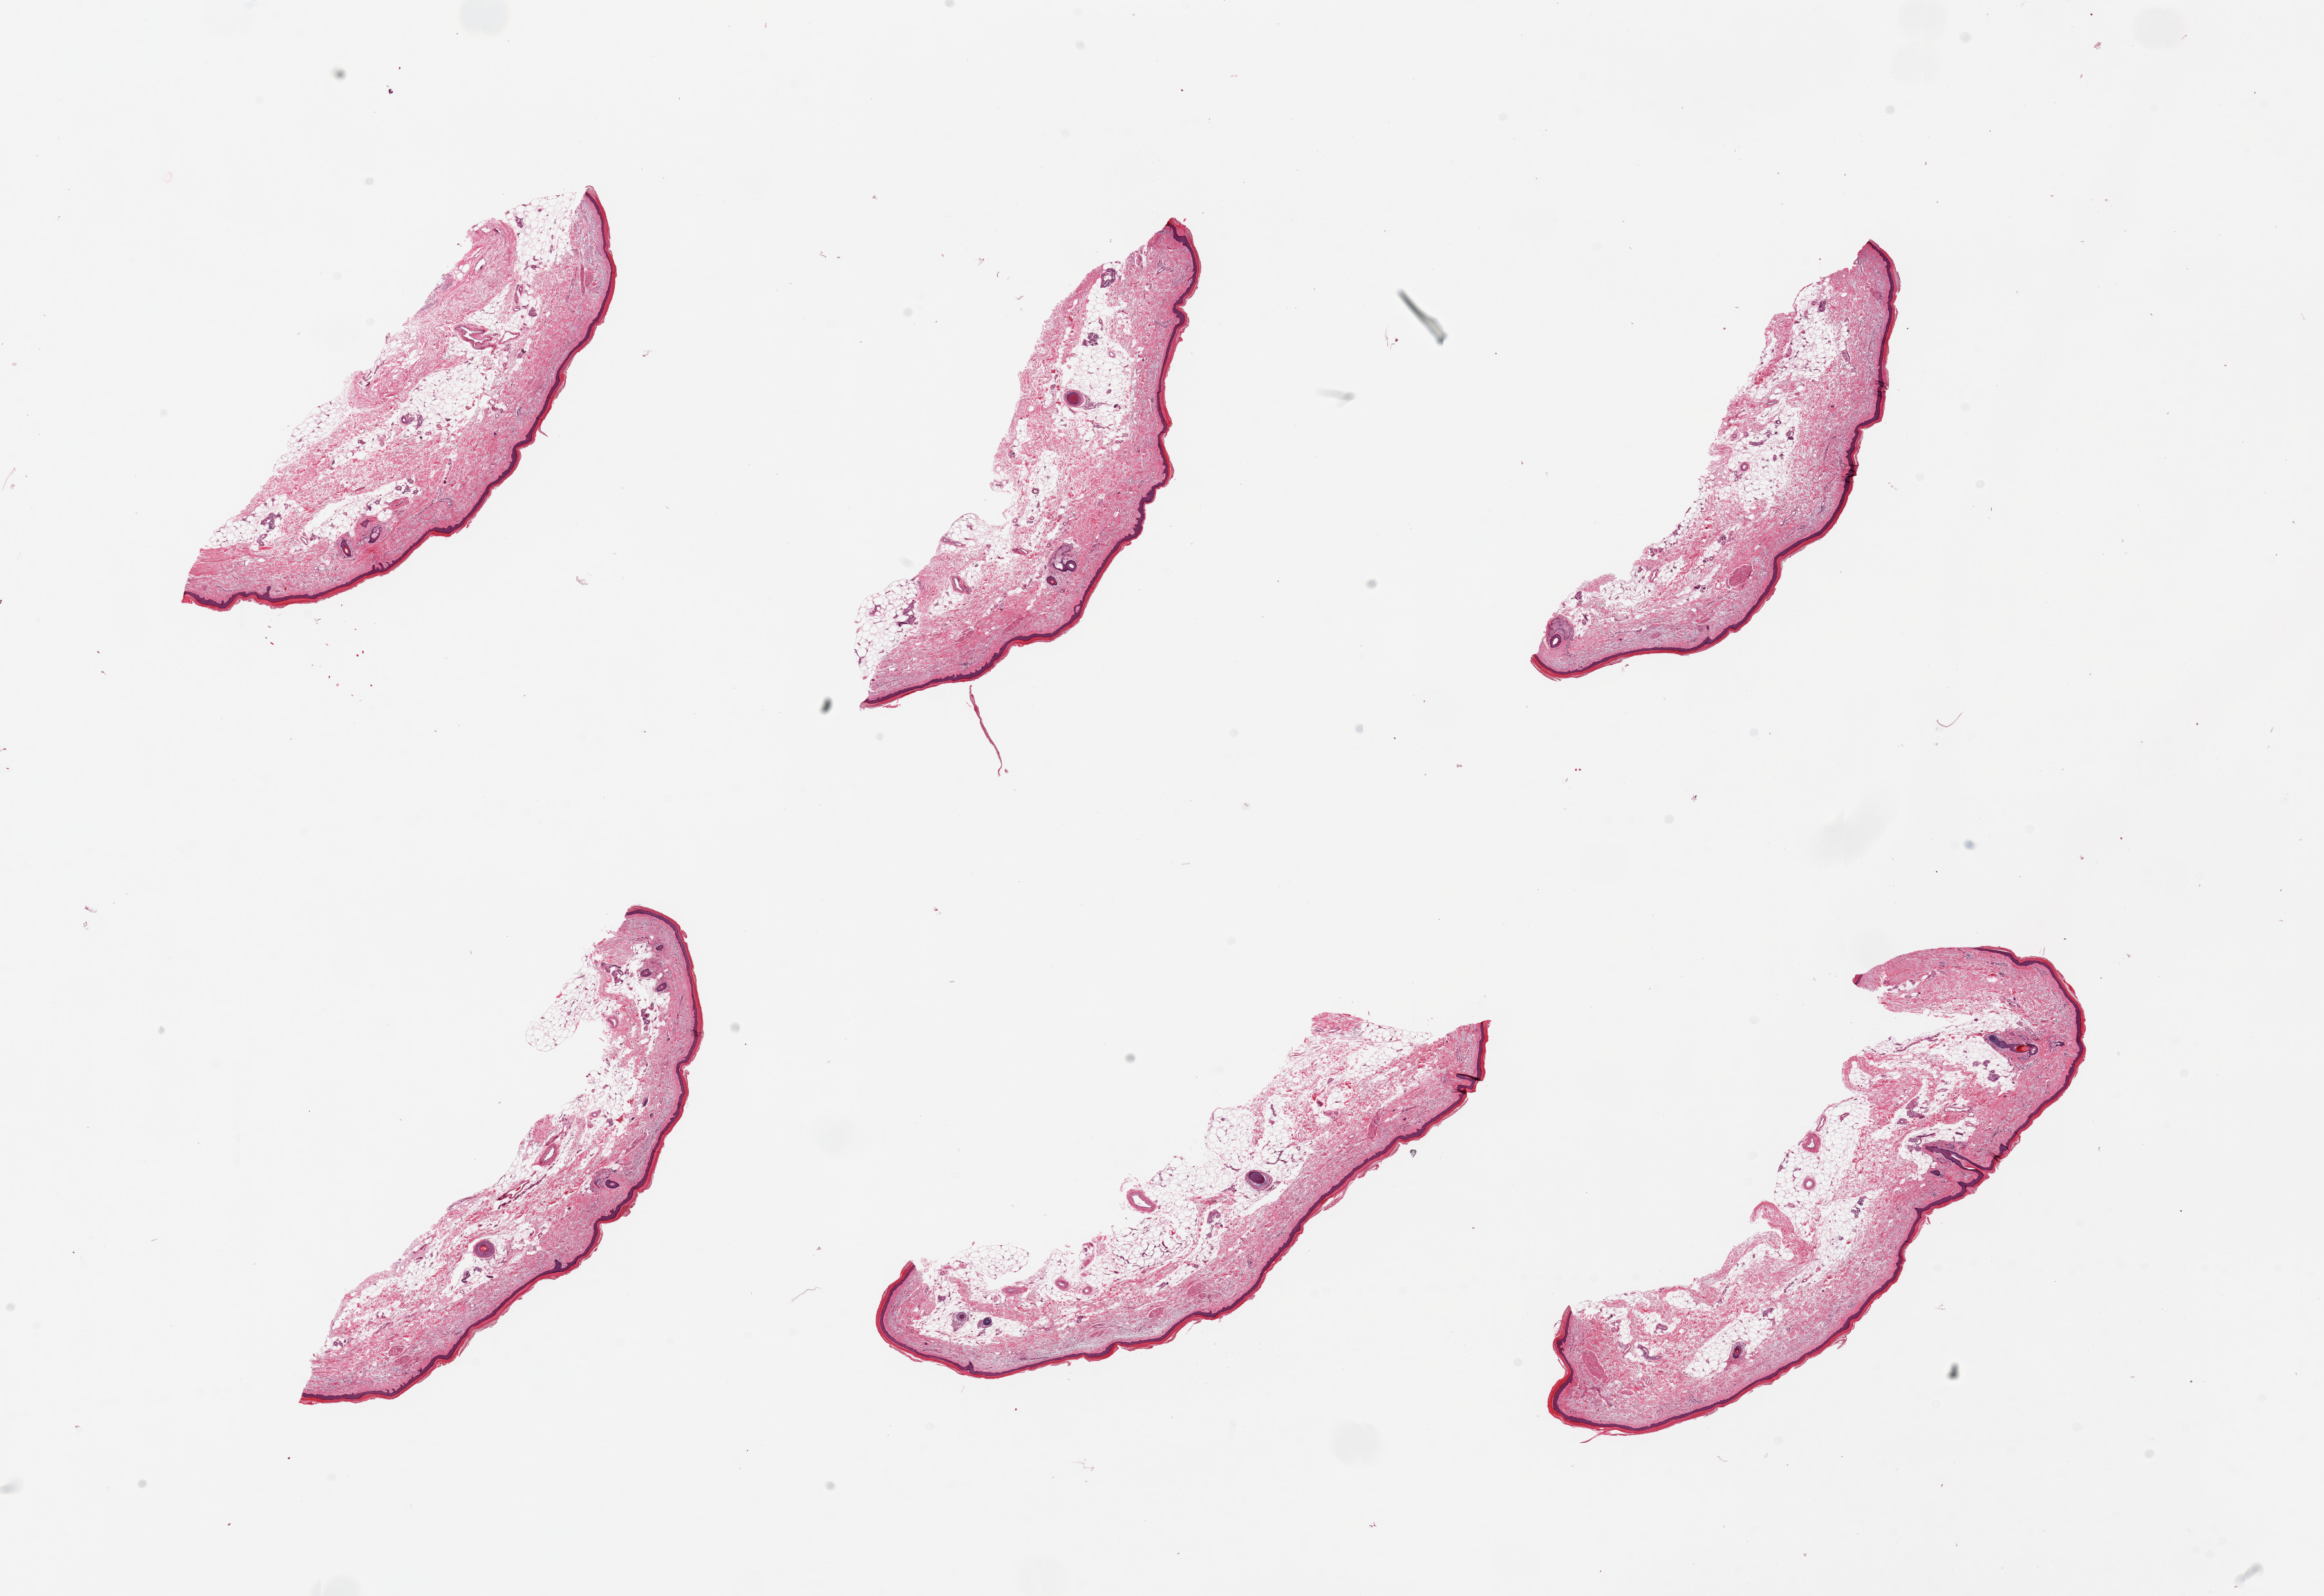
Whole-slide image, haematoxylin and eosin stain, whole scanned area (about 28.5 x 19.6 mm, acquisition: 20x scan) shown as a low-resolution overview. PAXgene-fixed paraffin-embedded (PFPE) section. Section of skin of lower leg (target tissue). Tissue donor sample. Donor sex: female.
• review note (as recorded): 6 pieces, minimal dermal fat; squamous epithelium is ~80 microns thick